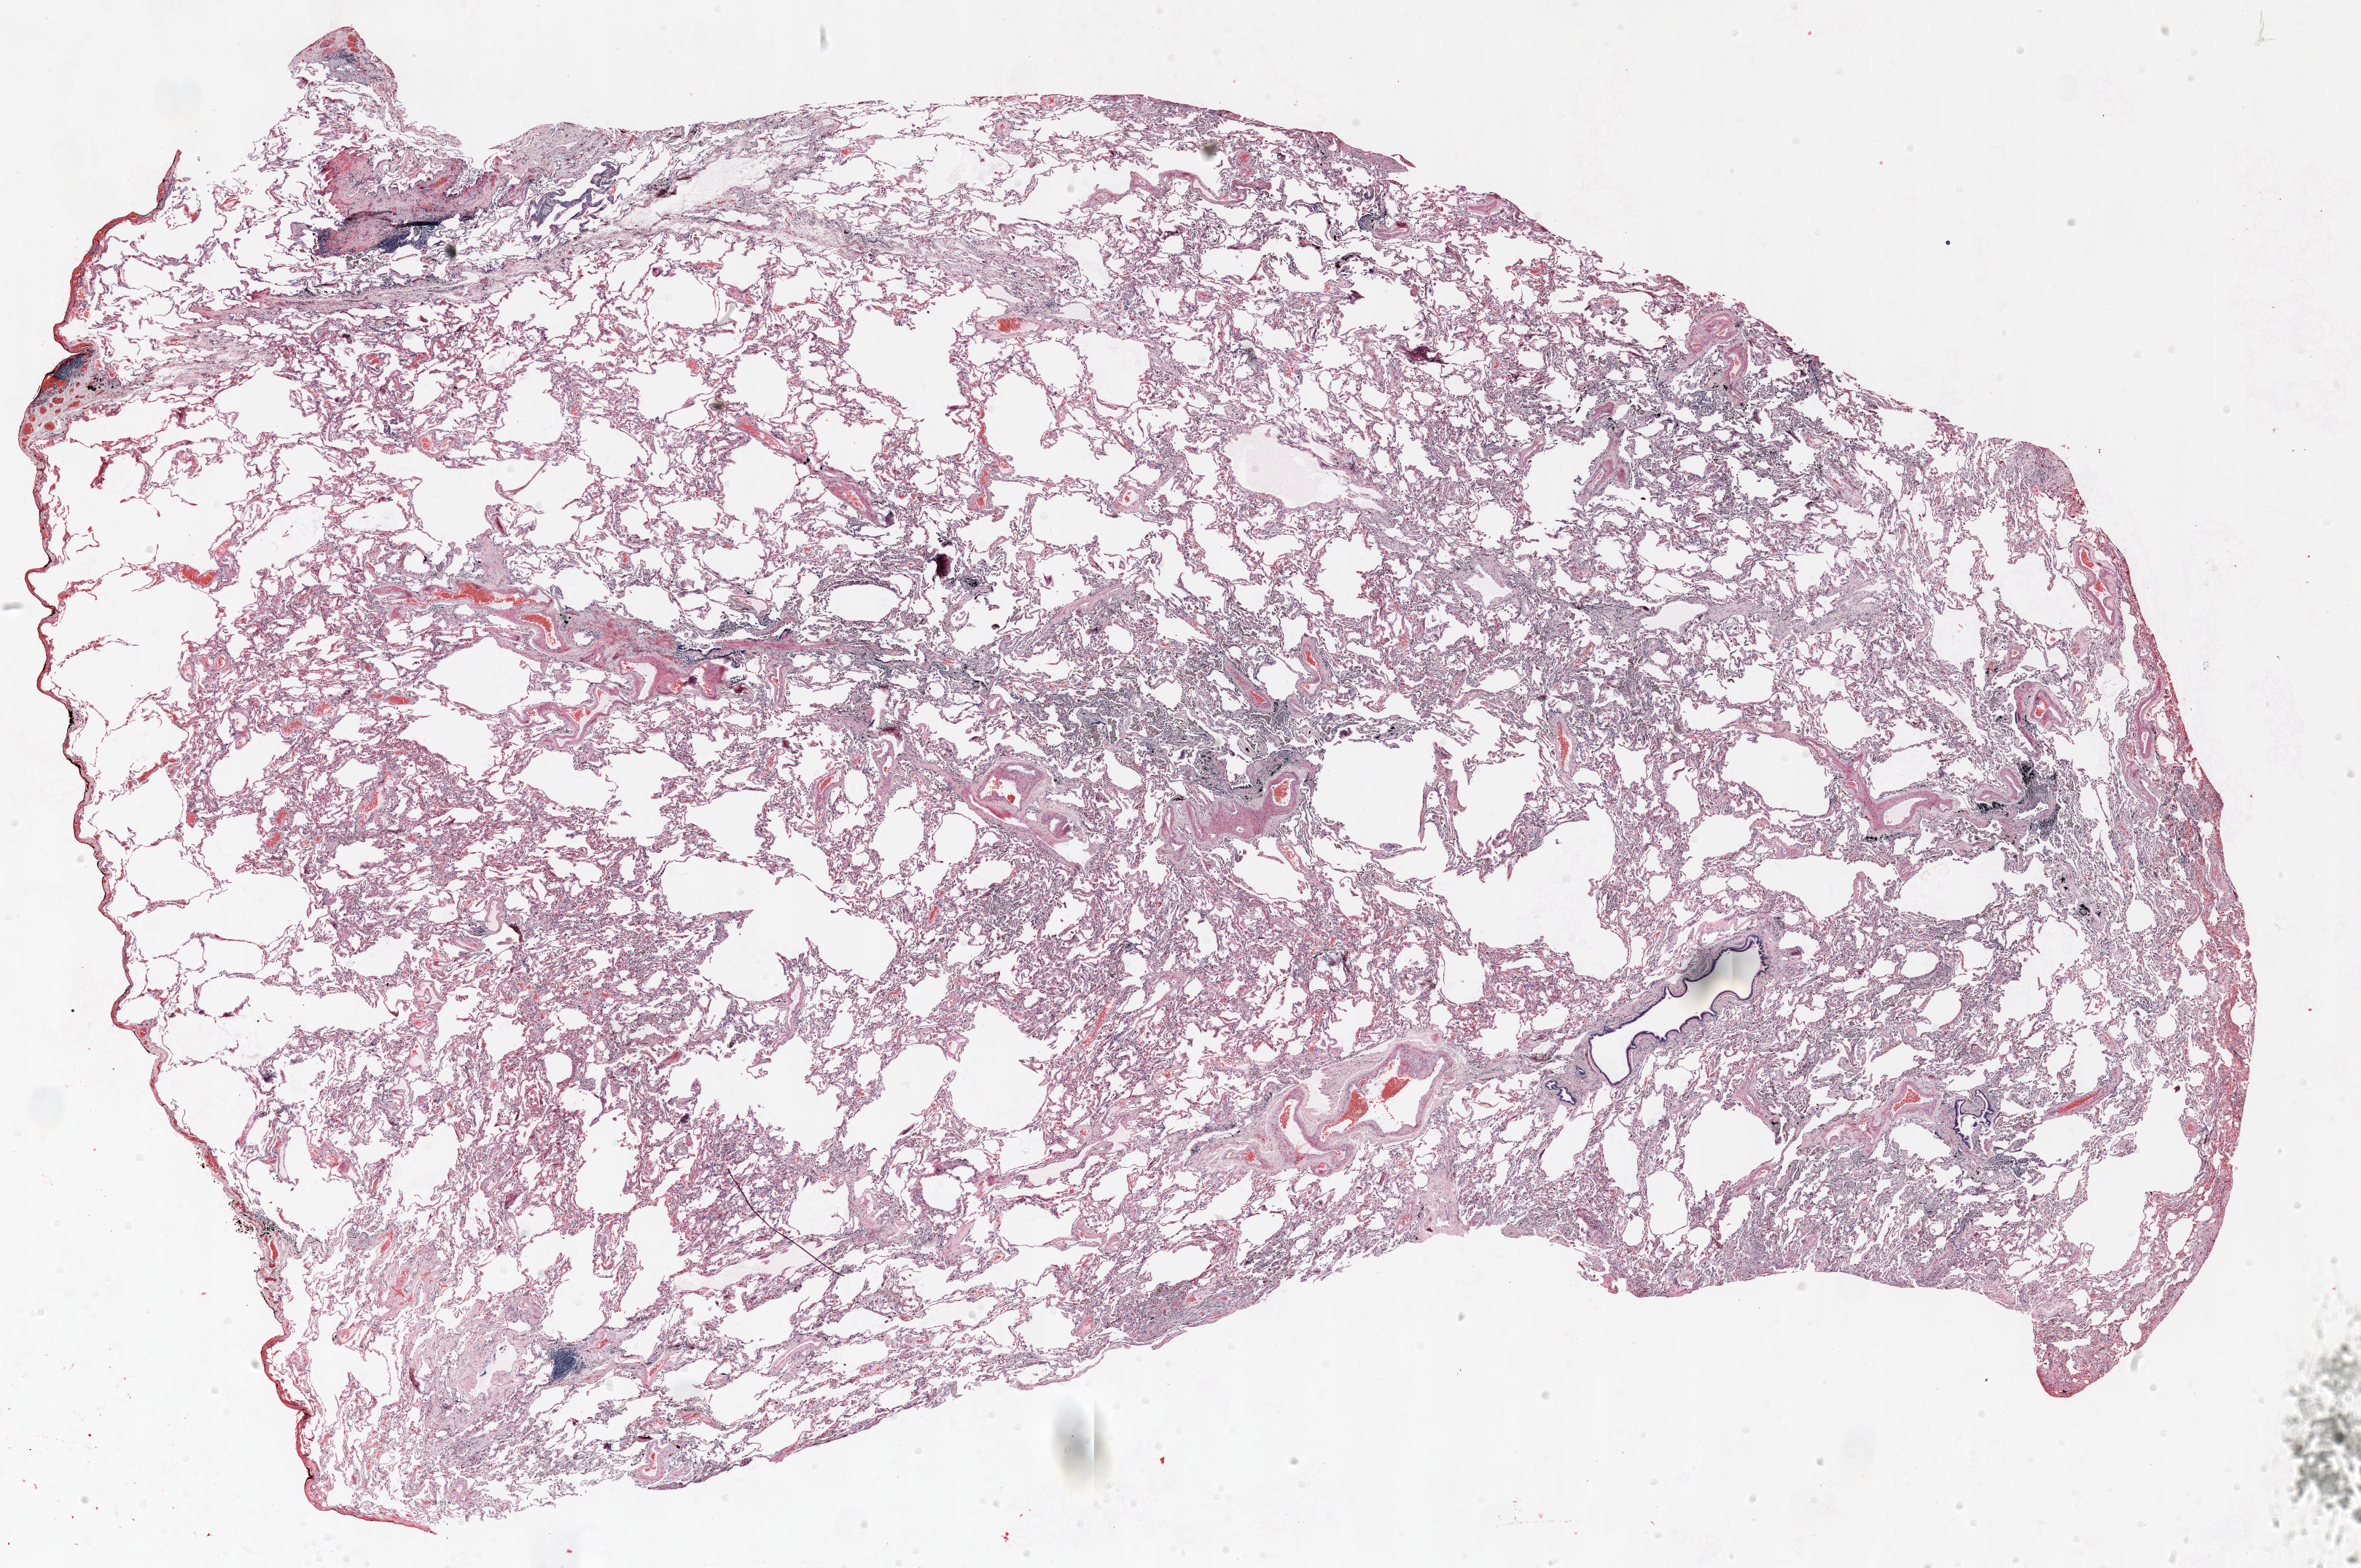
Whole-slide histology image, Hematoxylin and eosin (H&E) stained — whole scanned area (about 26.0 x 17.3 mm, slide scanned at 20x) shown as a low-resolution overview, formalin-fixed paraffin-embedded (FFPE) section, lung. Male patient, aged 70 at enrolment. Current smoker at enrolment. Grade: poorly differentiated (G3).
* primary tumour location (clinical record): right upper lobe
* participant's lung-cancer diagnosis: Adenocarcinoma, NOS
* stage (AJCC 6th edition): IIA
* tumour size (pathology): 23 mm